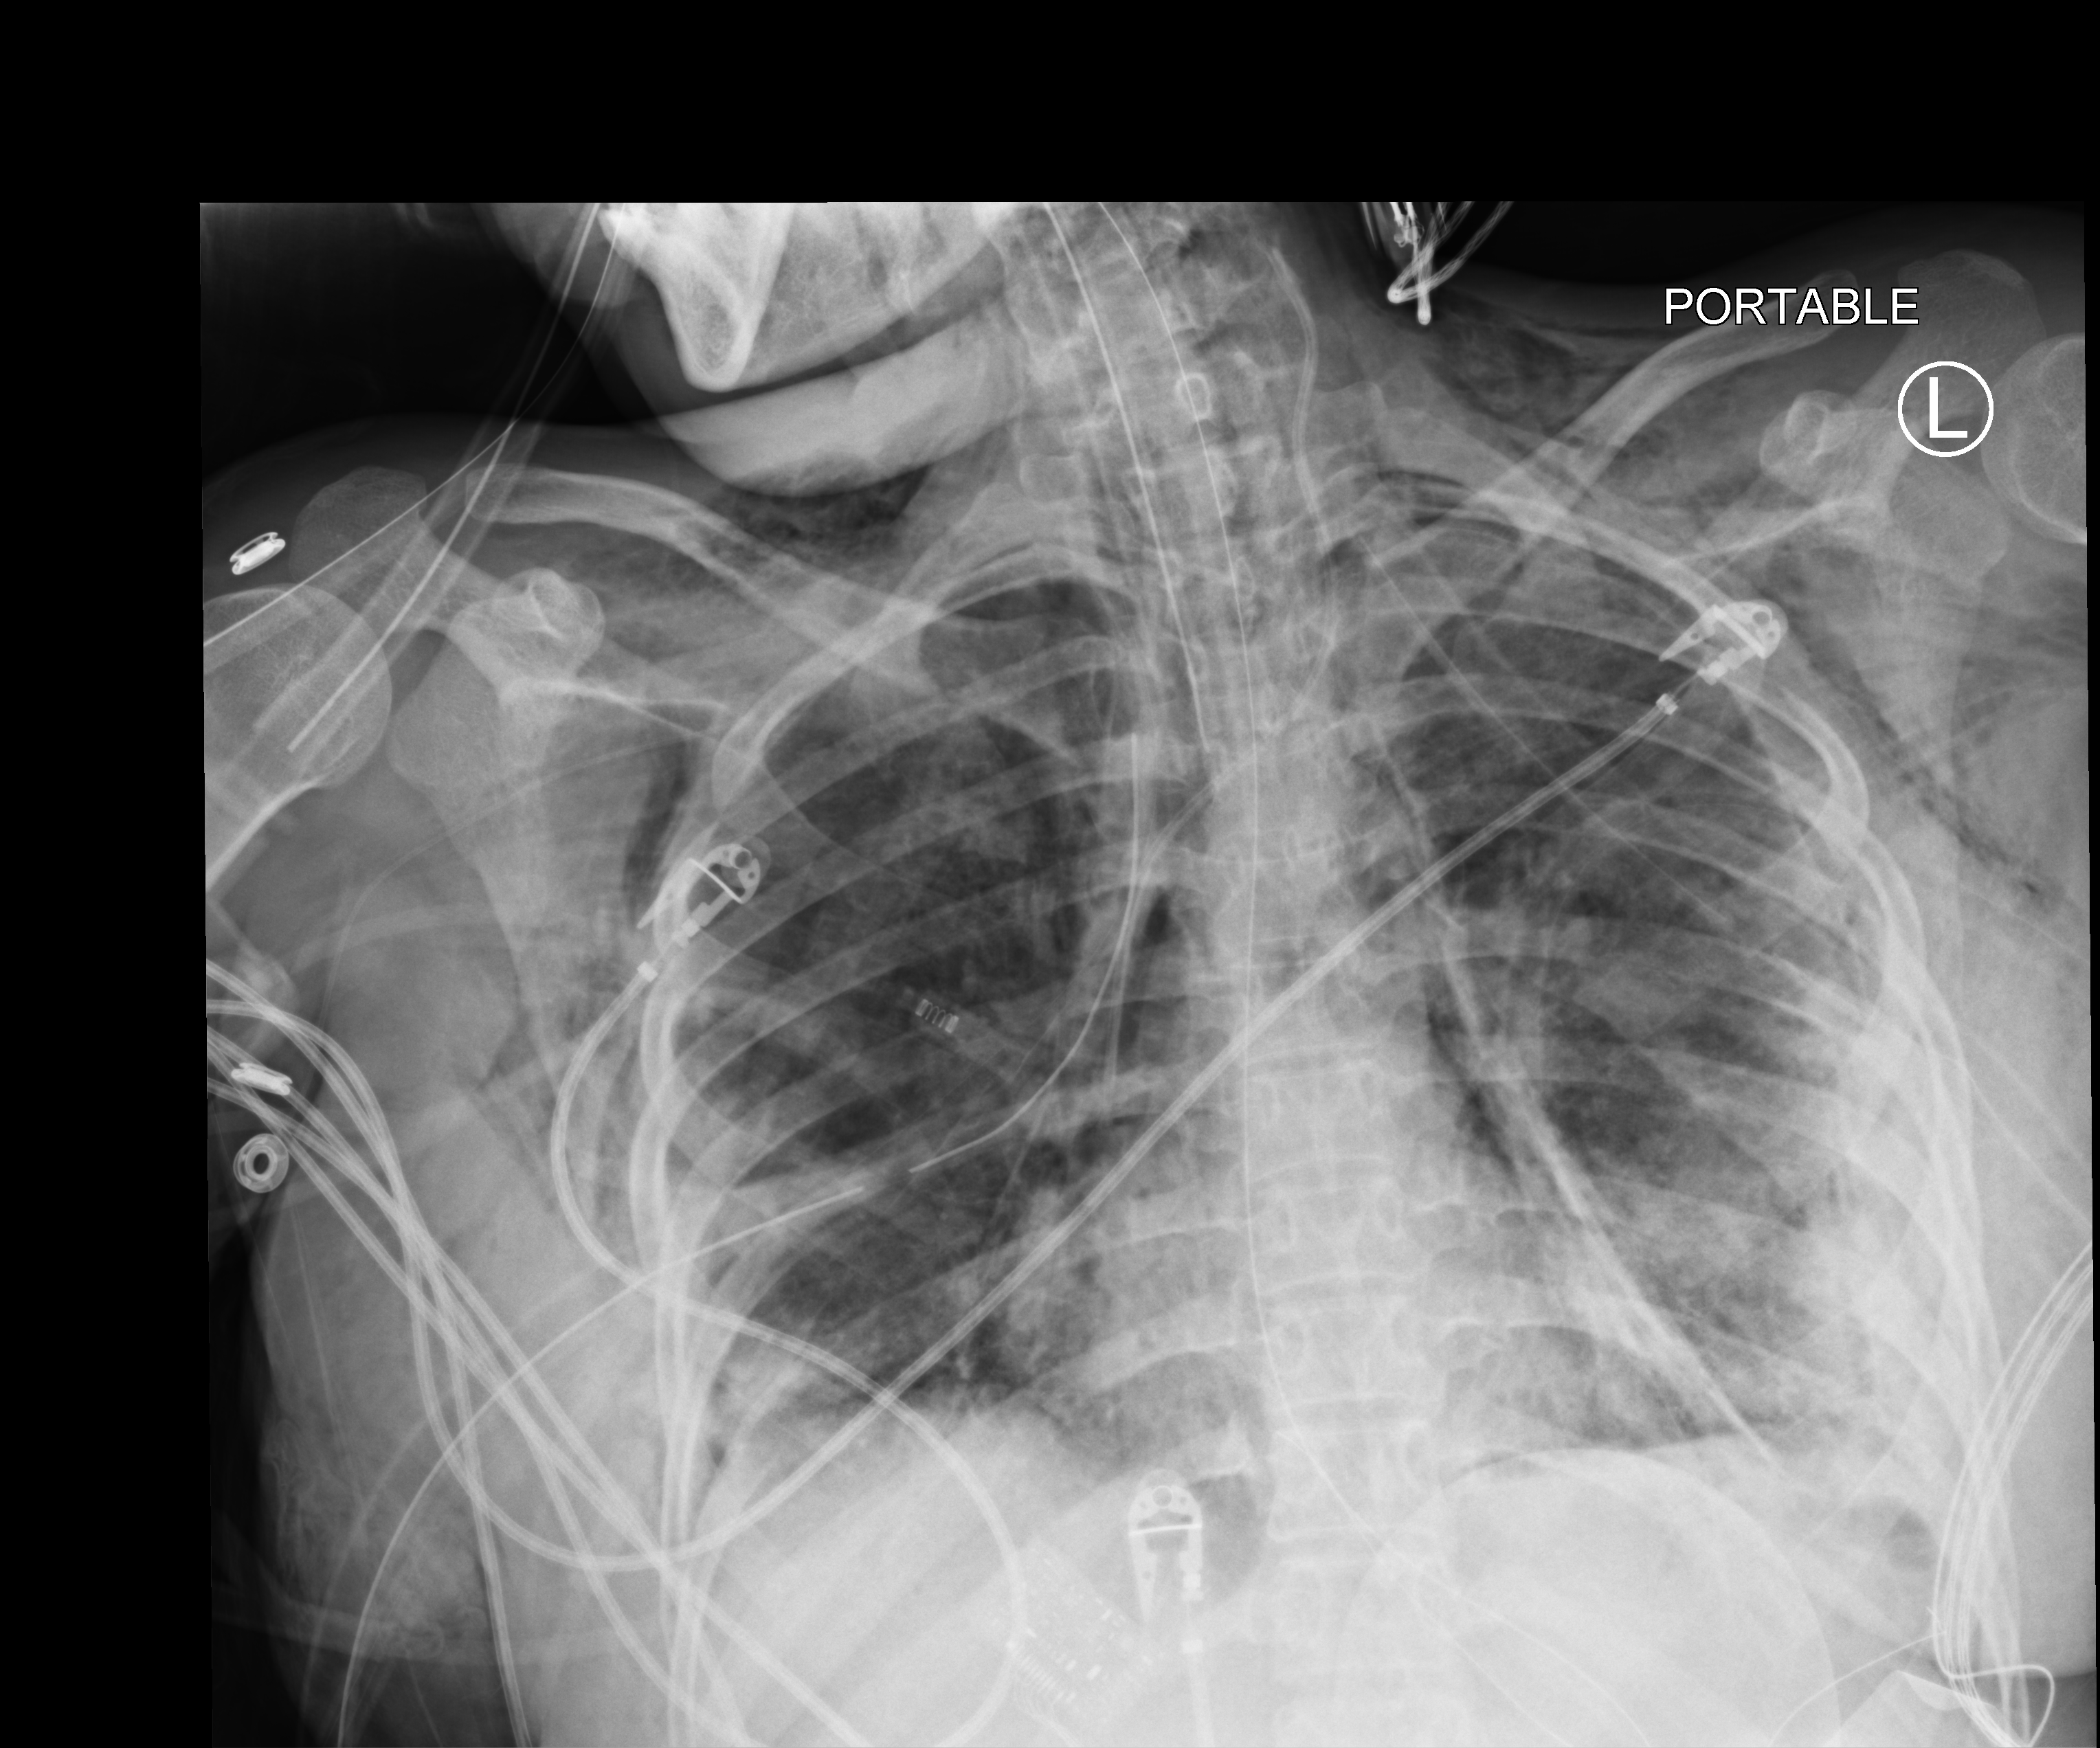
Bedside chest radiograph (computed radiography); anteroposterior (AP) projection. Adult patient hospitalised with COVID-19, age 18–59 years.
Hospital-stay facts (about this admission, not read from this image; timing relative to this image not recorded):
- admitted to intensive care during this hospital stay: yes
- COPD (admission record): no